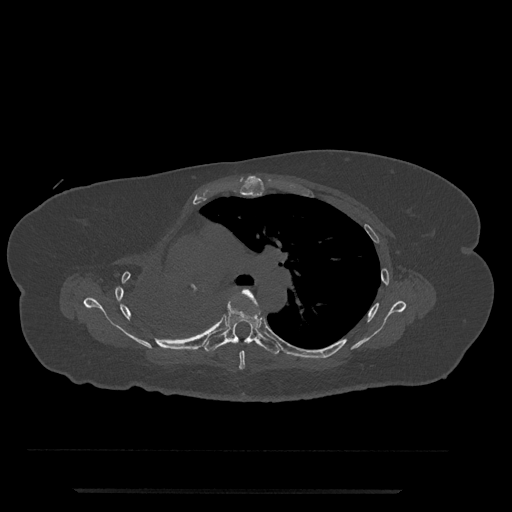
CT including the spine, one axial slice; position 512 of 797 along the scan axis; reconstruction kernel Br40s/3; 120 kVp; bone window (W 1800 / L 400 HU); 0.5 mm slice thickness; 512 × 512 image matrix, field of view 440 × 440 mm. Patient: female, 51 years. Case-level facts recorded for this patient, not image findings: primary cancer: neuro; vertebrae with lytic lesions (as recorded): T8.
Annotated regions visible in this slice (semi-automatic segmentation, software-assisted and operator-edited):
- T5 vertebra: box from (x=231, y=289) to (x=265, y=370) px
- T6 vertebra: (x=204, y=304)–(x=280, y=355)